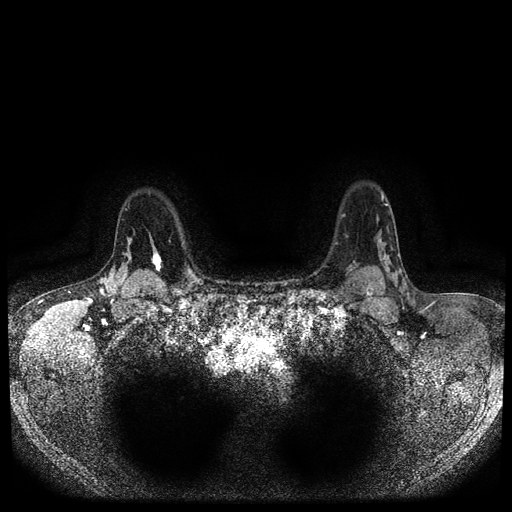
Breast MRI (dynamic contrast-enhanced, multi-phase), one axial slice. Slice 80 of 116 in the series (ordered by position). Dynamic contrast-enhanced series, time point 2 of 5 at this slice position (early post-contrast). 1.5 T. TE 2.6 ms, TR 5.4 ms. 512 × 512 image matrix. Female patient, age 47 years.
Annotated regions visible in this slice (semi-automatic segmentation, software-assisted and operator-edited):
- breast lesion (labelled 'tumour' in the annotation; benign lesions carry a separate 'benign' label): bounding box (x1, y1, x2, y2) in pixels: (149, 232, 163, 274)